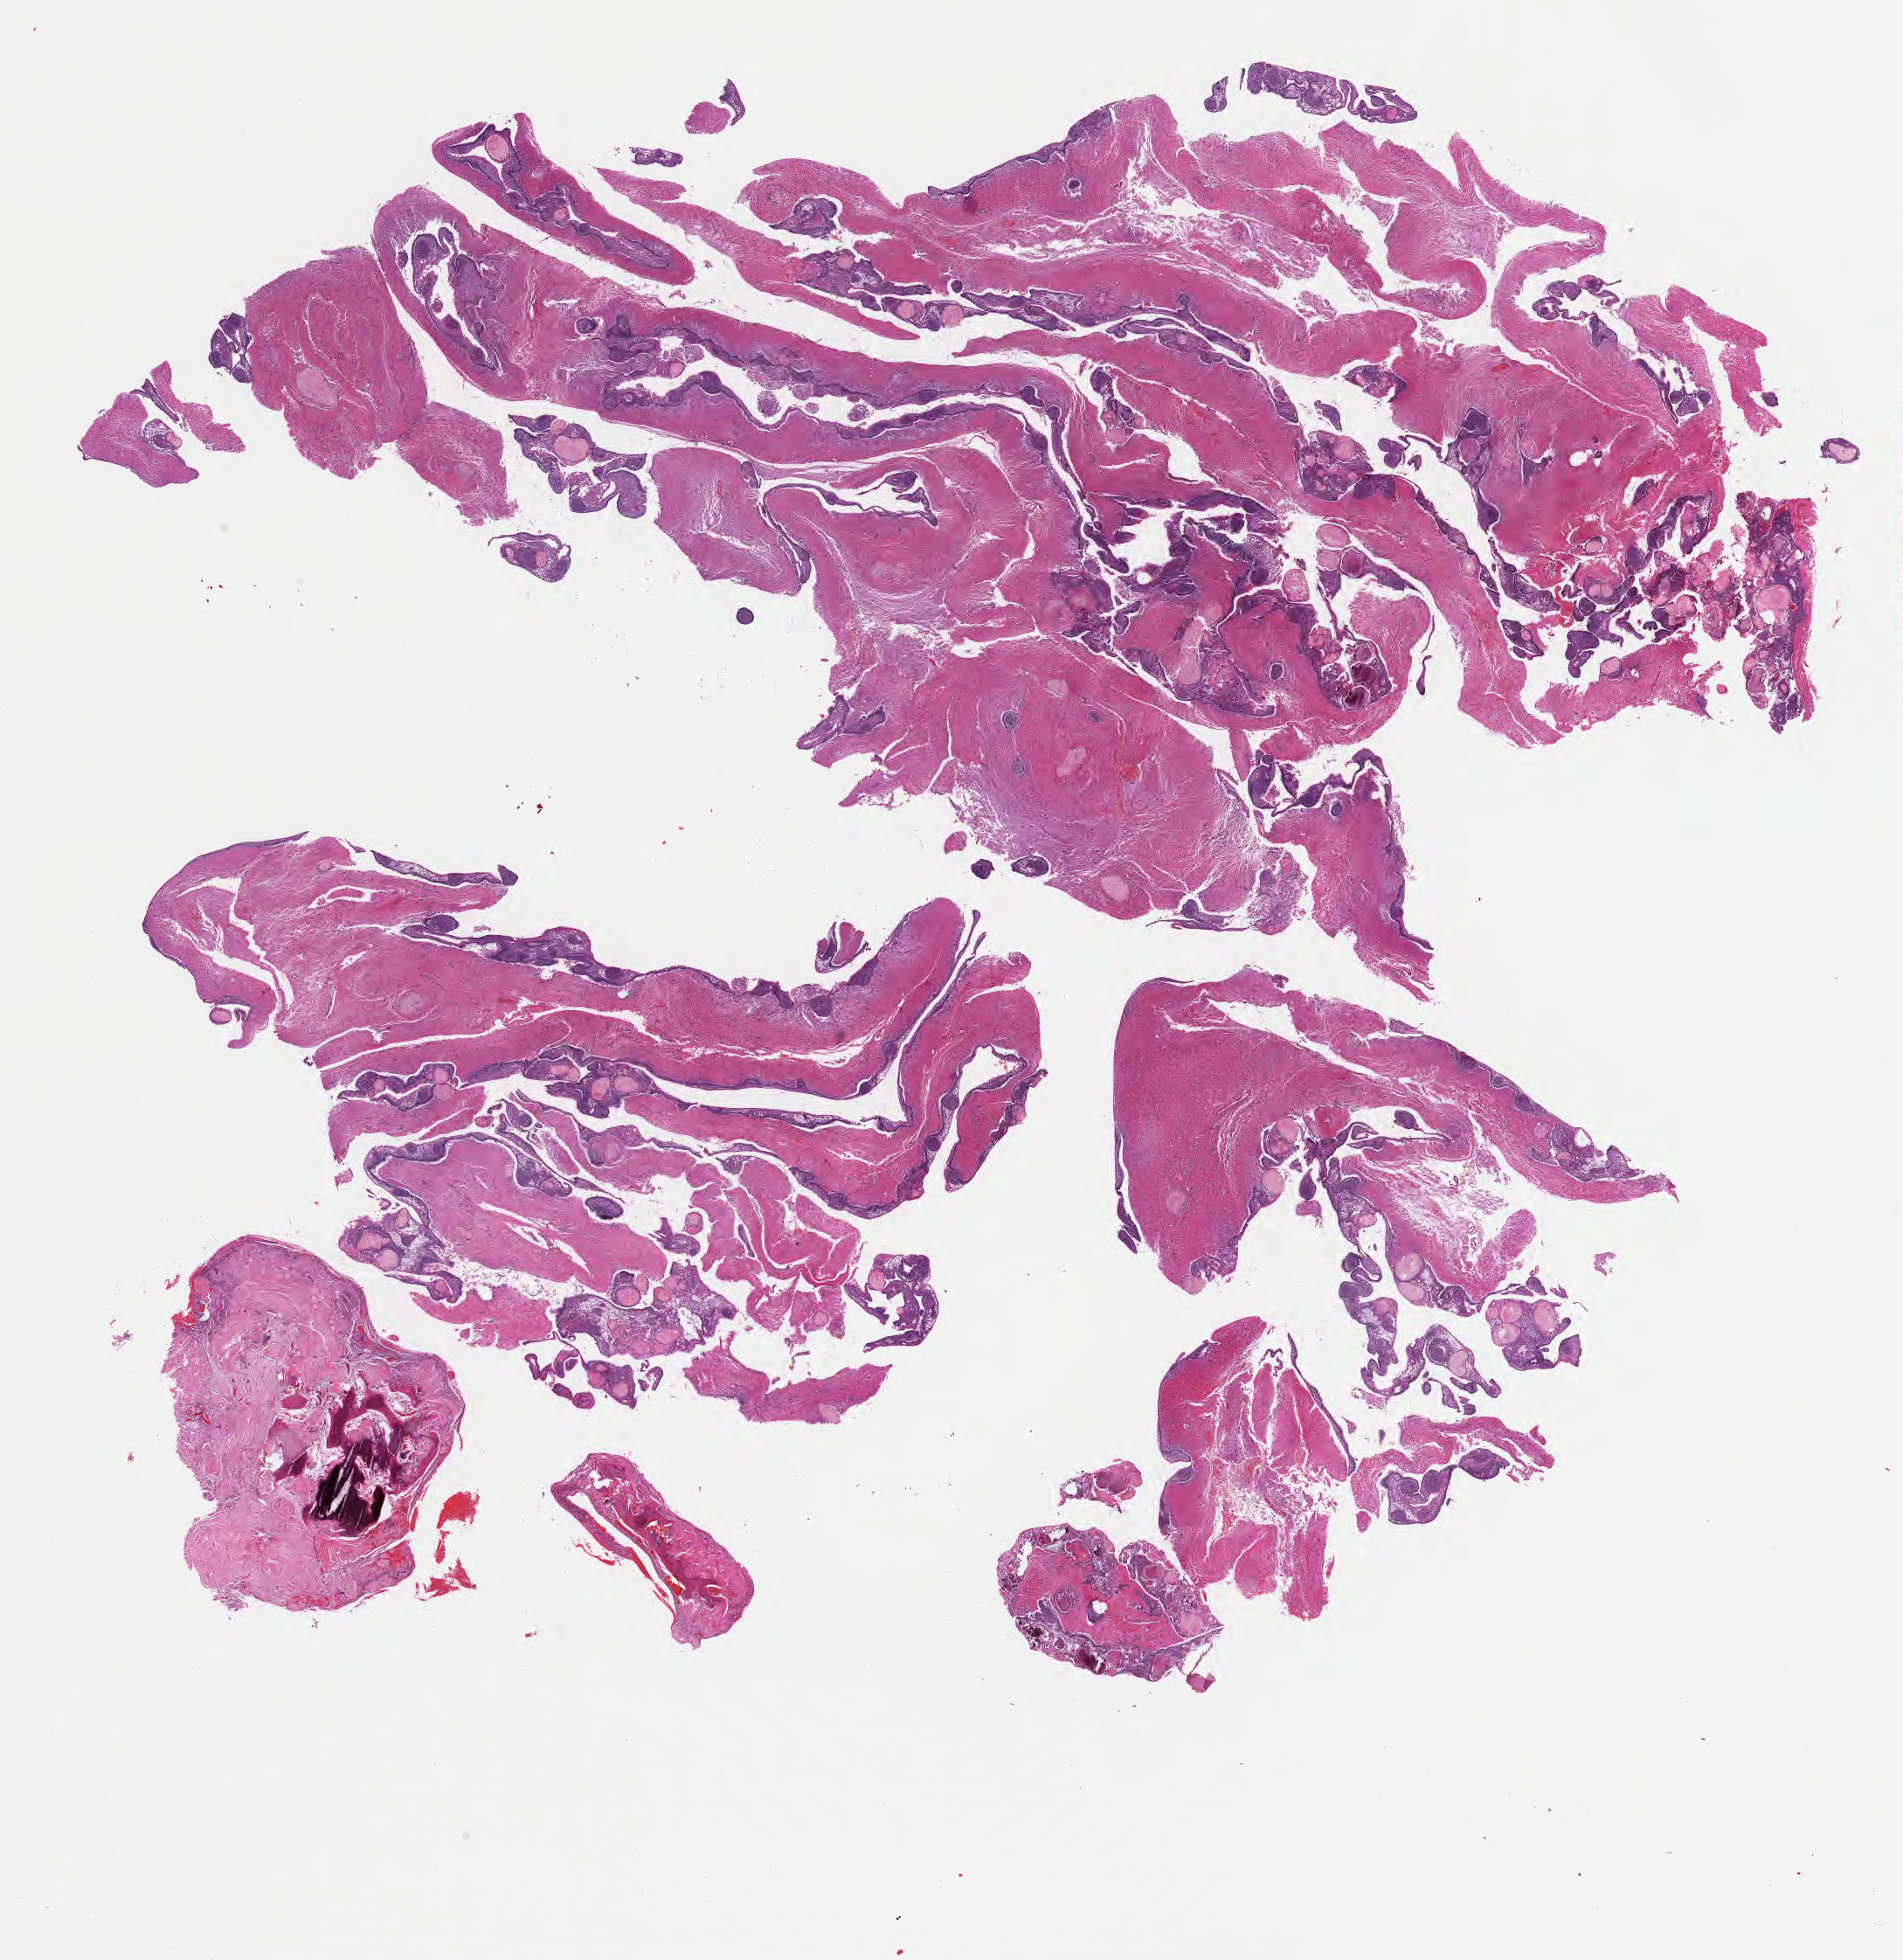
H&E whole-slide image of tumor tissue from the brain, shown as a low-resolution overview of the whole scanned area (about 17.6 x 18.1 mm); FFPE section. Patient: male, age 47 months (3 years 11 months).
- diagnosis: Craniopharyngioma, adamantinomatous